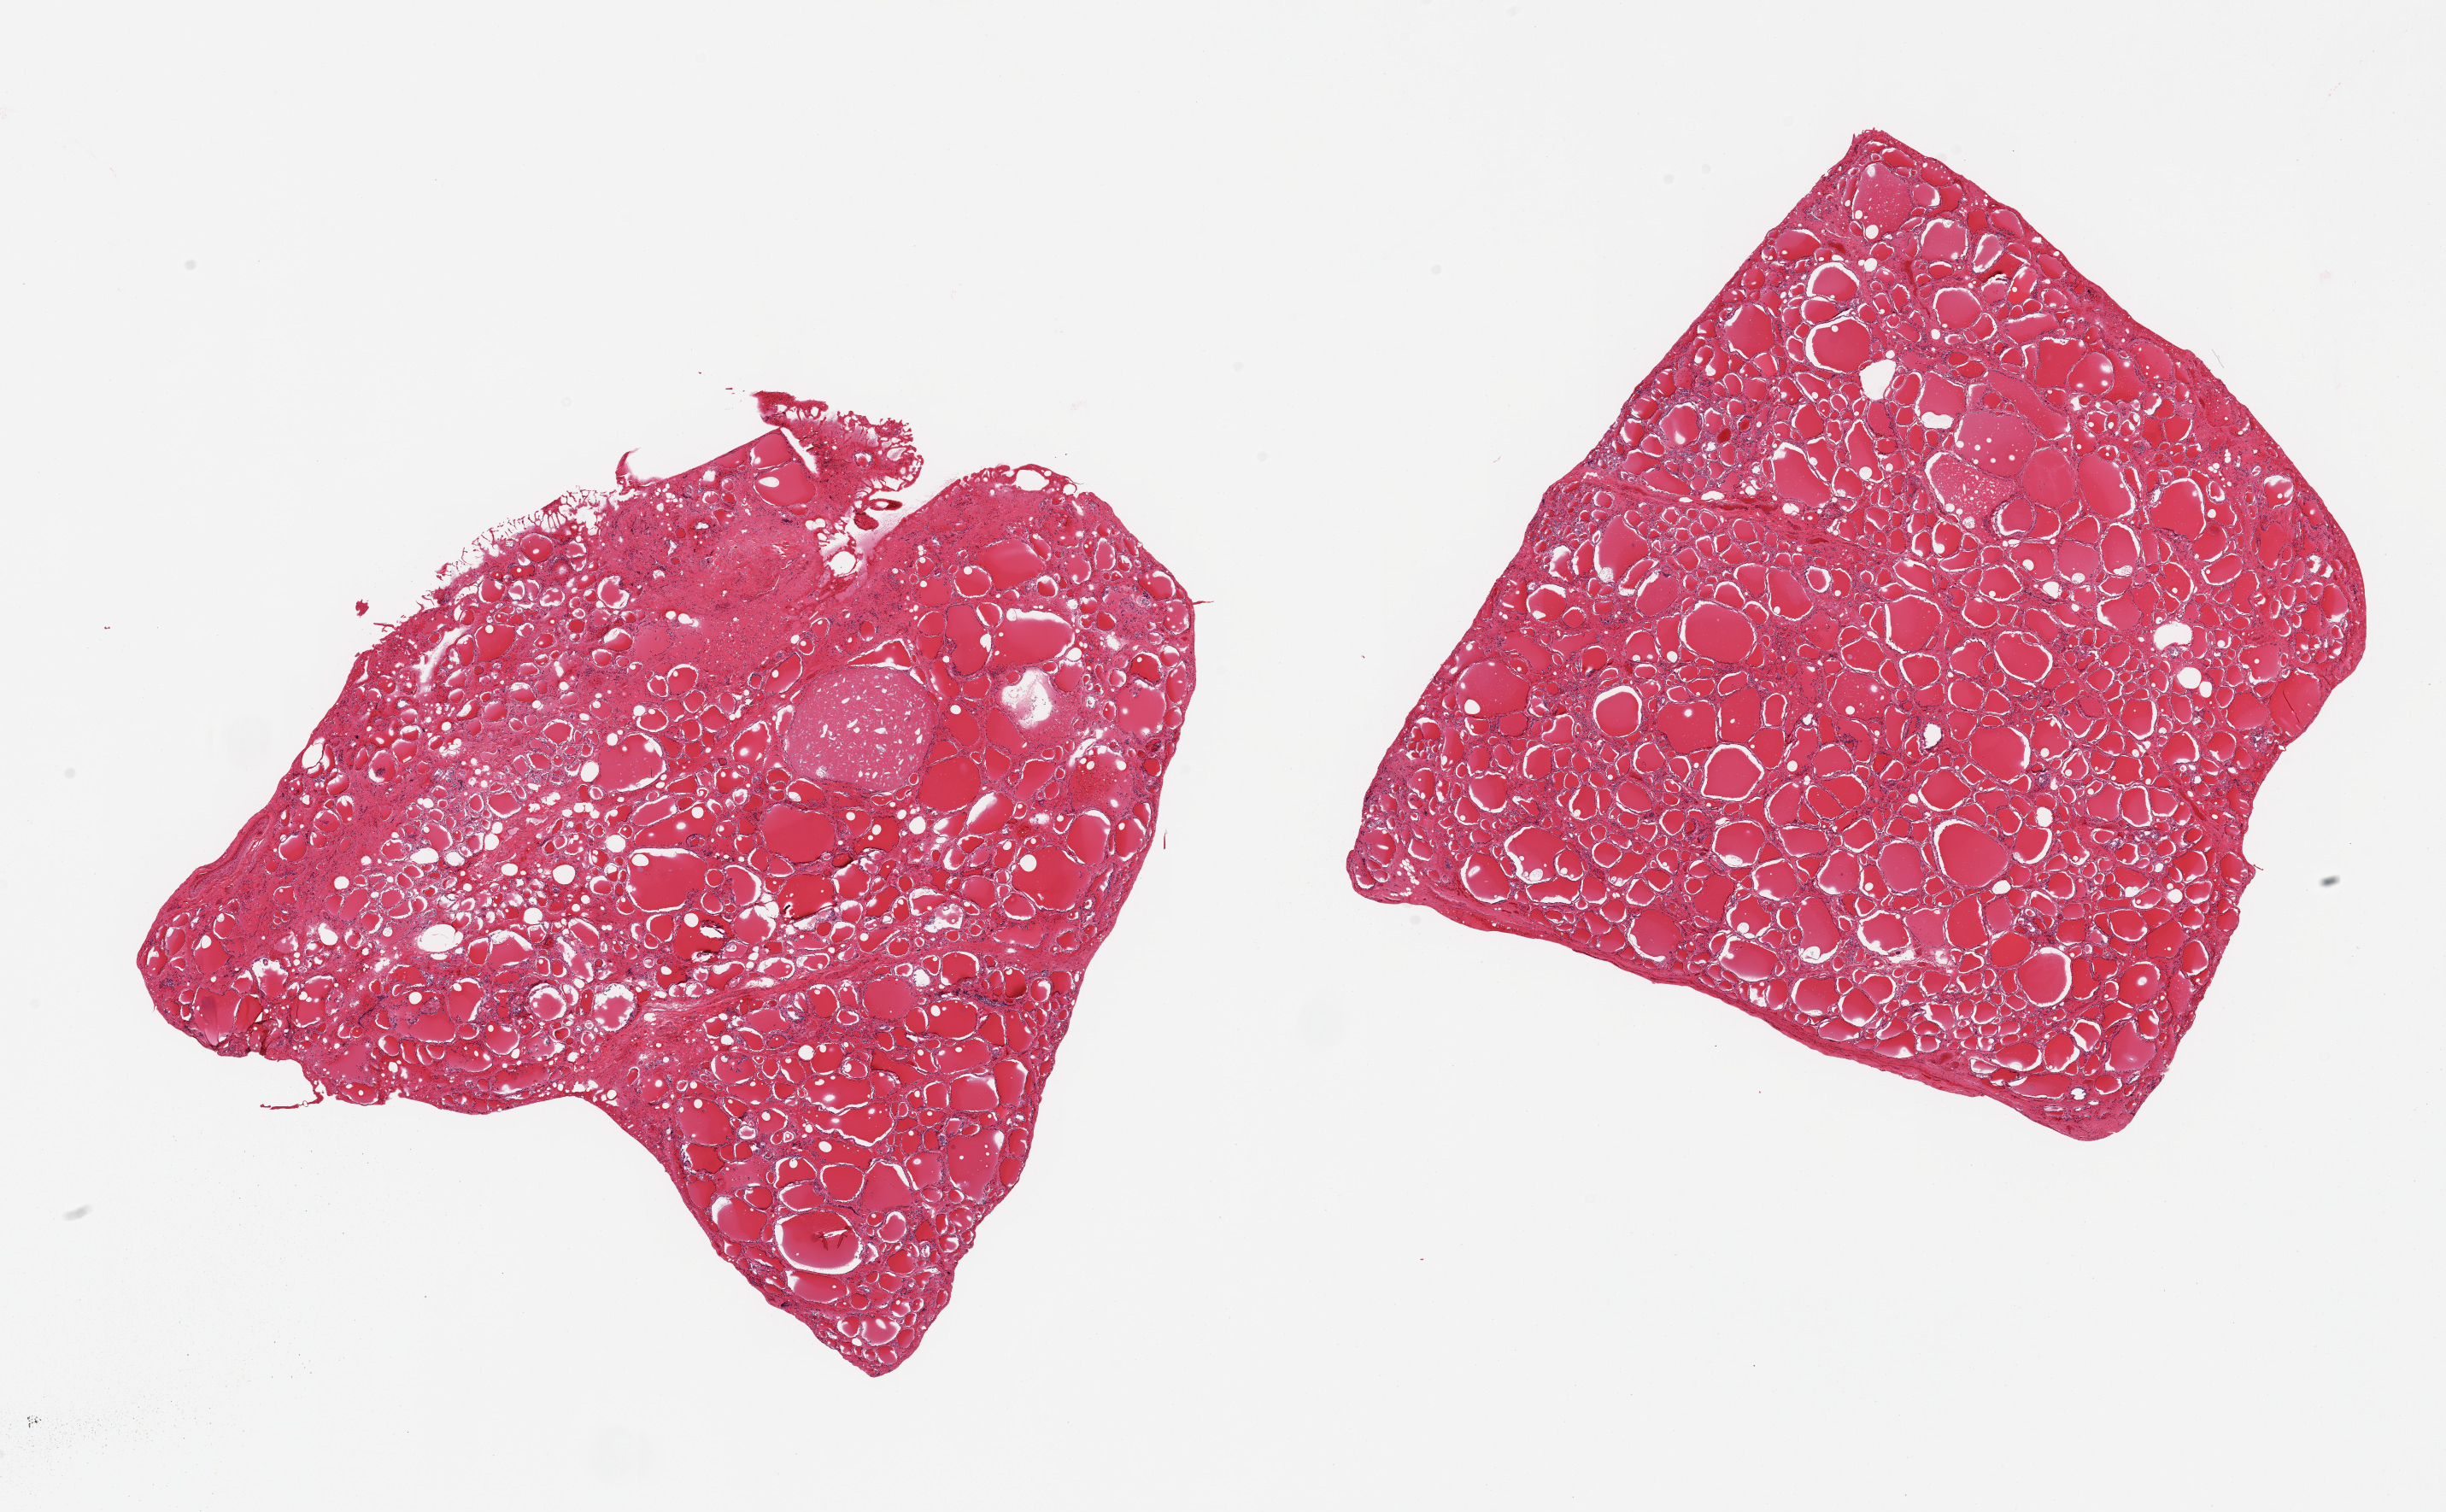
Digitized hematoxylin and eosin (H&E)-stained section, shown as a low-resolution overview of the whole scanned area (about 22.6 x 14.0 mm). PAXgene-fixed paraffin-embedded (PFPE) section. Target tissue: thyroid. Donor tissue sample.
Review note (as recorded): 2 pieces, ~1mm incidental ciolloid cyst, no abnormalities.